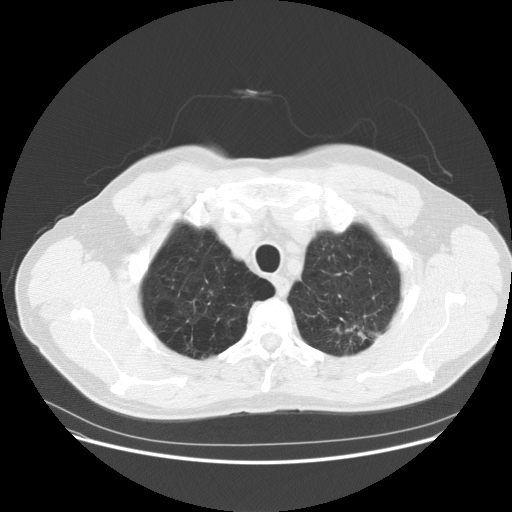
Low-dose screening chest CT, one axial slice; position 142 of 158 along the scan axis; reconstruction kernel STANDARD; 120 kVp; lung window (W 1500 / L -600 HU); 2.5 mm slice thickness; 512 × 512 image matrix.
Outlined on this slice (manually delineated by an expert):
- lesion 1 (tumor, upper lobe of left lung): bounding box <345,324,368,342> (left, top, right, bottom; pixels)